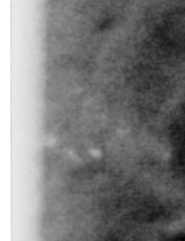
Region of interest cut from a scanned film mammogram (one marked finding), right breast, MLO view, BI-RADS breast density category 3 (scale 1–4).
Marked abnormality: calcifications, morphology pleomorphic, distribution clustered; BI-RADS assessment category 4; pathology (as recorded): benign.